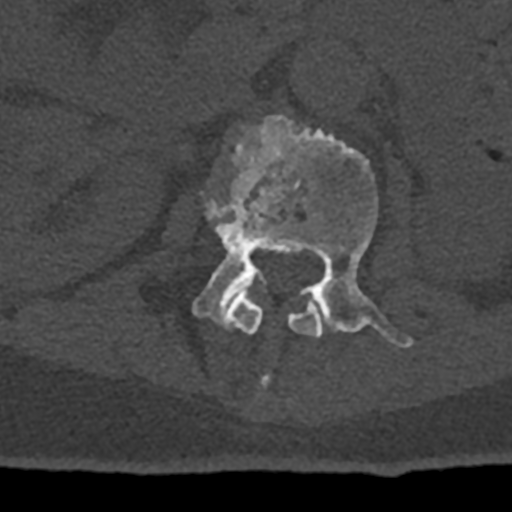
CT including the spine, one axial slice. Position 397 of 797 along the scan axis. Reconstruction kernel Br40s/3. 120 kVp. Bone window (W 1800 / L 400 HU). 0.5 mm slice thickness. 512 × 512 image matrix. Male patient, age 74 years. From the clinical record (not read from this slice): primary cancer: renal; vertebrae with lytic lesions (as recorded): T10, L1, L2, L3, L4, L5.
Outlined on this slice (semi-automatic segmentation, software-assisted and operator-edited):
- L1 vertebra: bounding box [x1, y1, x2, y2] px = [207, 199, 321, 389]
- L2 vertebra: [192, 114, 413, 348]